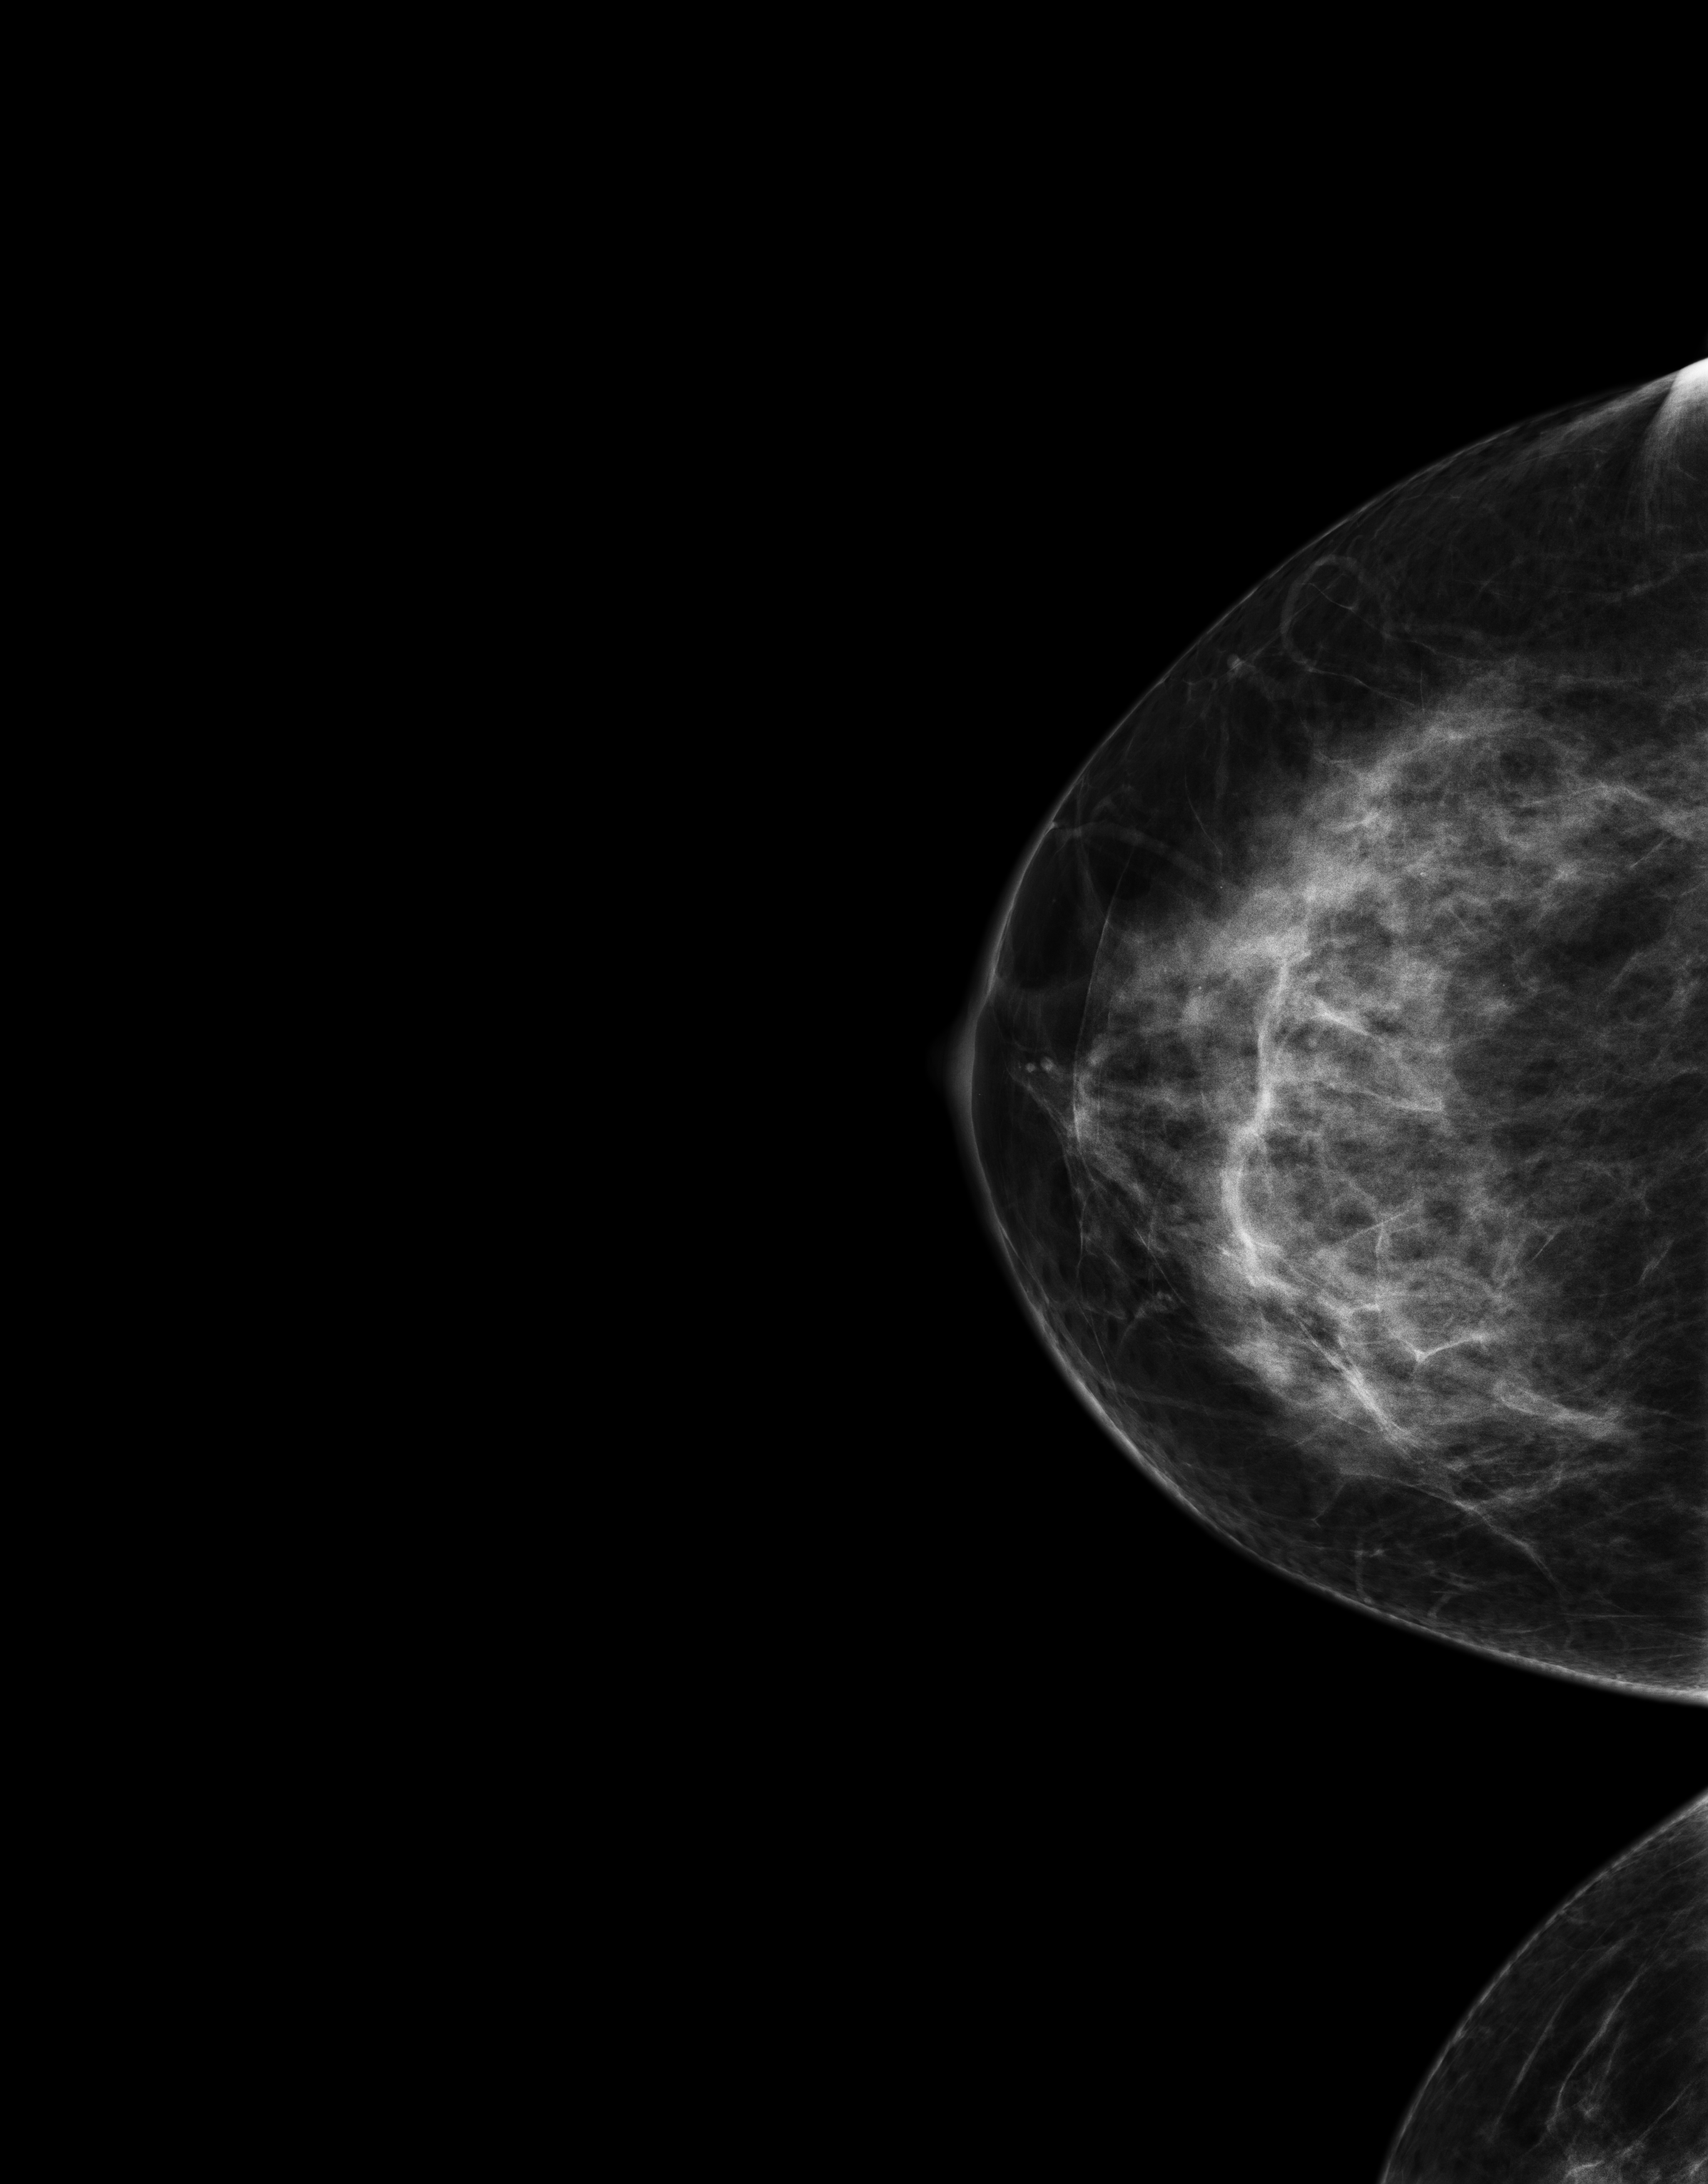
Digital mammogram (FFDM), right breast, cranio-caudal projection, annual screening mammography examination, compressed breast thickness 75 mm, system: Senographe Essential ADS_56.21.3. Female patient, age 44 years.
- breast density at the screening exam (both breasts): heterogeneously dense (BI-RADS density category c)
- final BI-RADS assessment for this screening round (tomosynthesis exam, both breasts): category 1
- recall: no recall after this screen